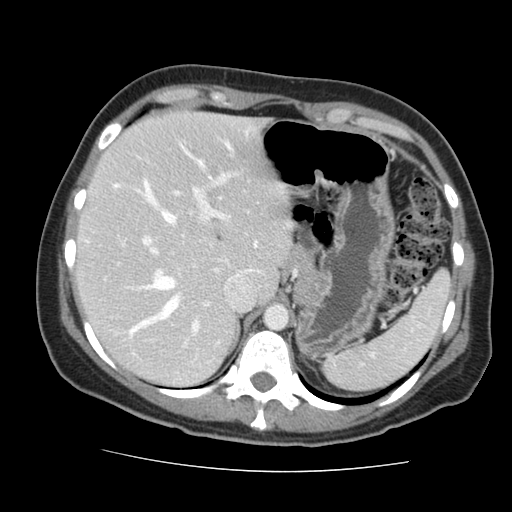
Contrast-enhanced abdominal CT, one axial slice; slice 108 of 144 in the series (ordered by position); 120 kVp; soft-tissue window (W 400 / L 40 HU); 2.5 mm slice thickness; 512 × 512 image matrix. Female patient, age 46 years. From the clinical record (not read from this slice): diagnosis: colorectal cancer liver metastases, imaged before liver resection; multiple liver metastases: no.
Structures marked on this image (expert manual segmentation):
- hepatic veins: bounding box <113,180,179,318> (left, top, right, bottom; pixels)
- liver: <79,113,288,385>
- planned liver remnant (the part of the liver to remain after resection): <79,113,288,385>
- portal vein (with intrahepatic branches): <129,174,229,336>